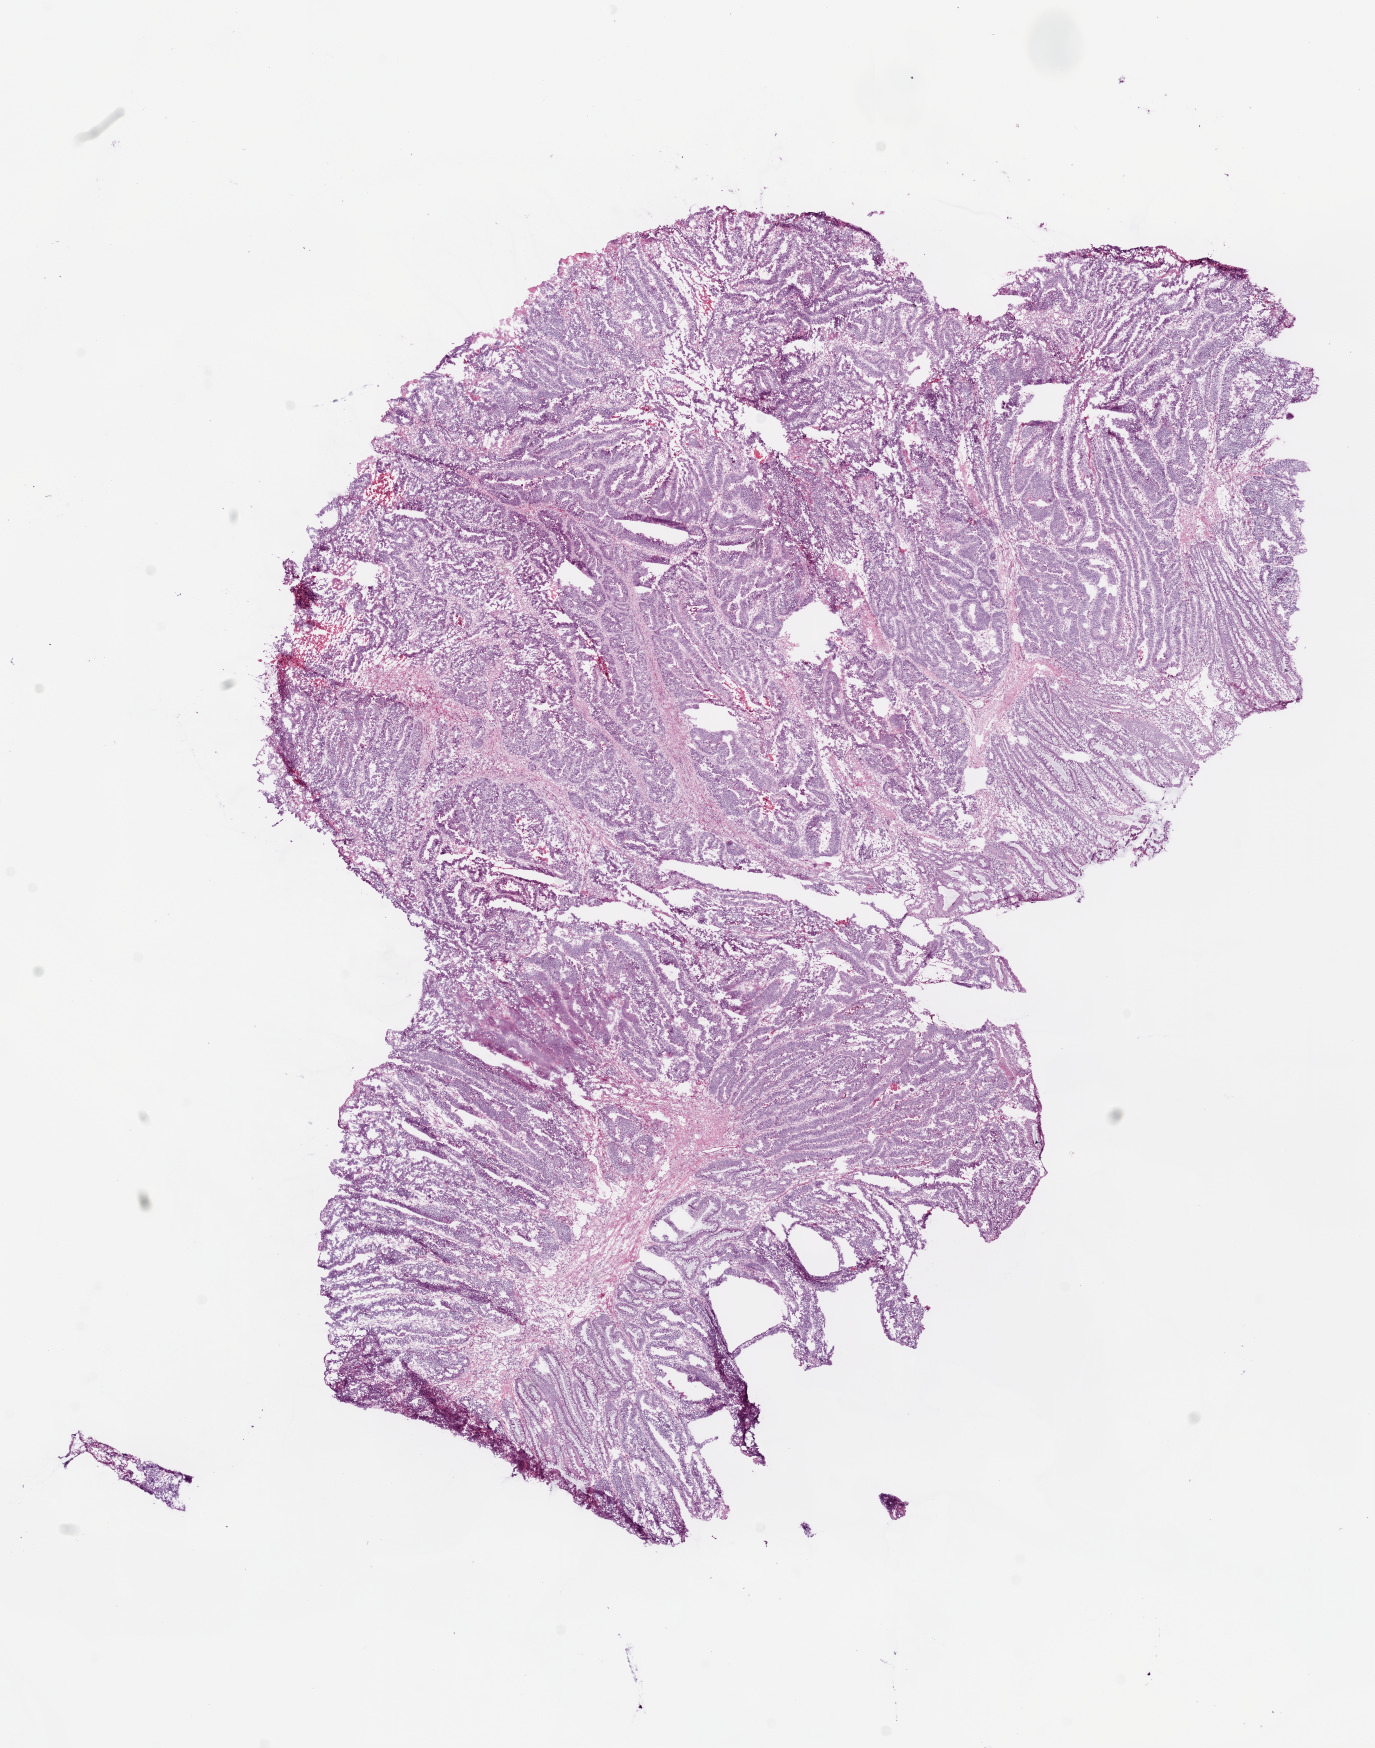
Whole-slide histology image, H&E — low-resolution overview of the scanned area, about 11.0 x 14.0 mm (acquisition: 20x scan). Frozen section. Colon, primary tumour sample. Male, age 63 years at initial diagnosis. Pathologist review of this section (percent, as recorded): tumour cells 90%, tumour nuclei 90%, normal cells 0%, stromal cells 10%, necrosis 0%.
AJCC pathologic stage: III (5th edition). Lymph nodes positive (case pathology): 3 of 43 examined. Histologic diagnosis: Adenocarcinoma, NOS. TNM: T3 N1 M0.